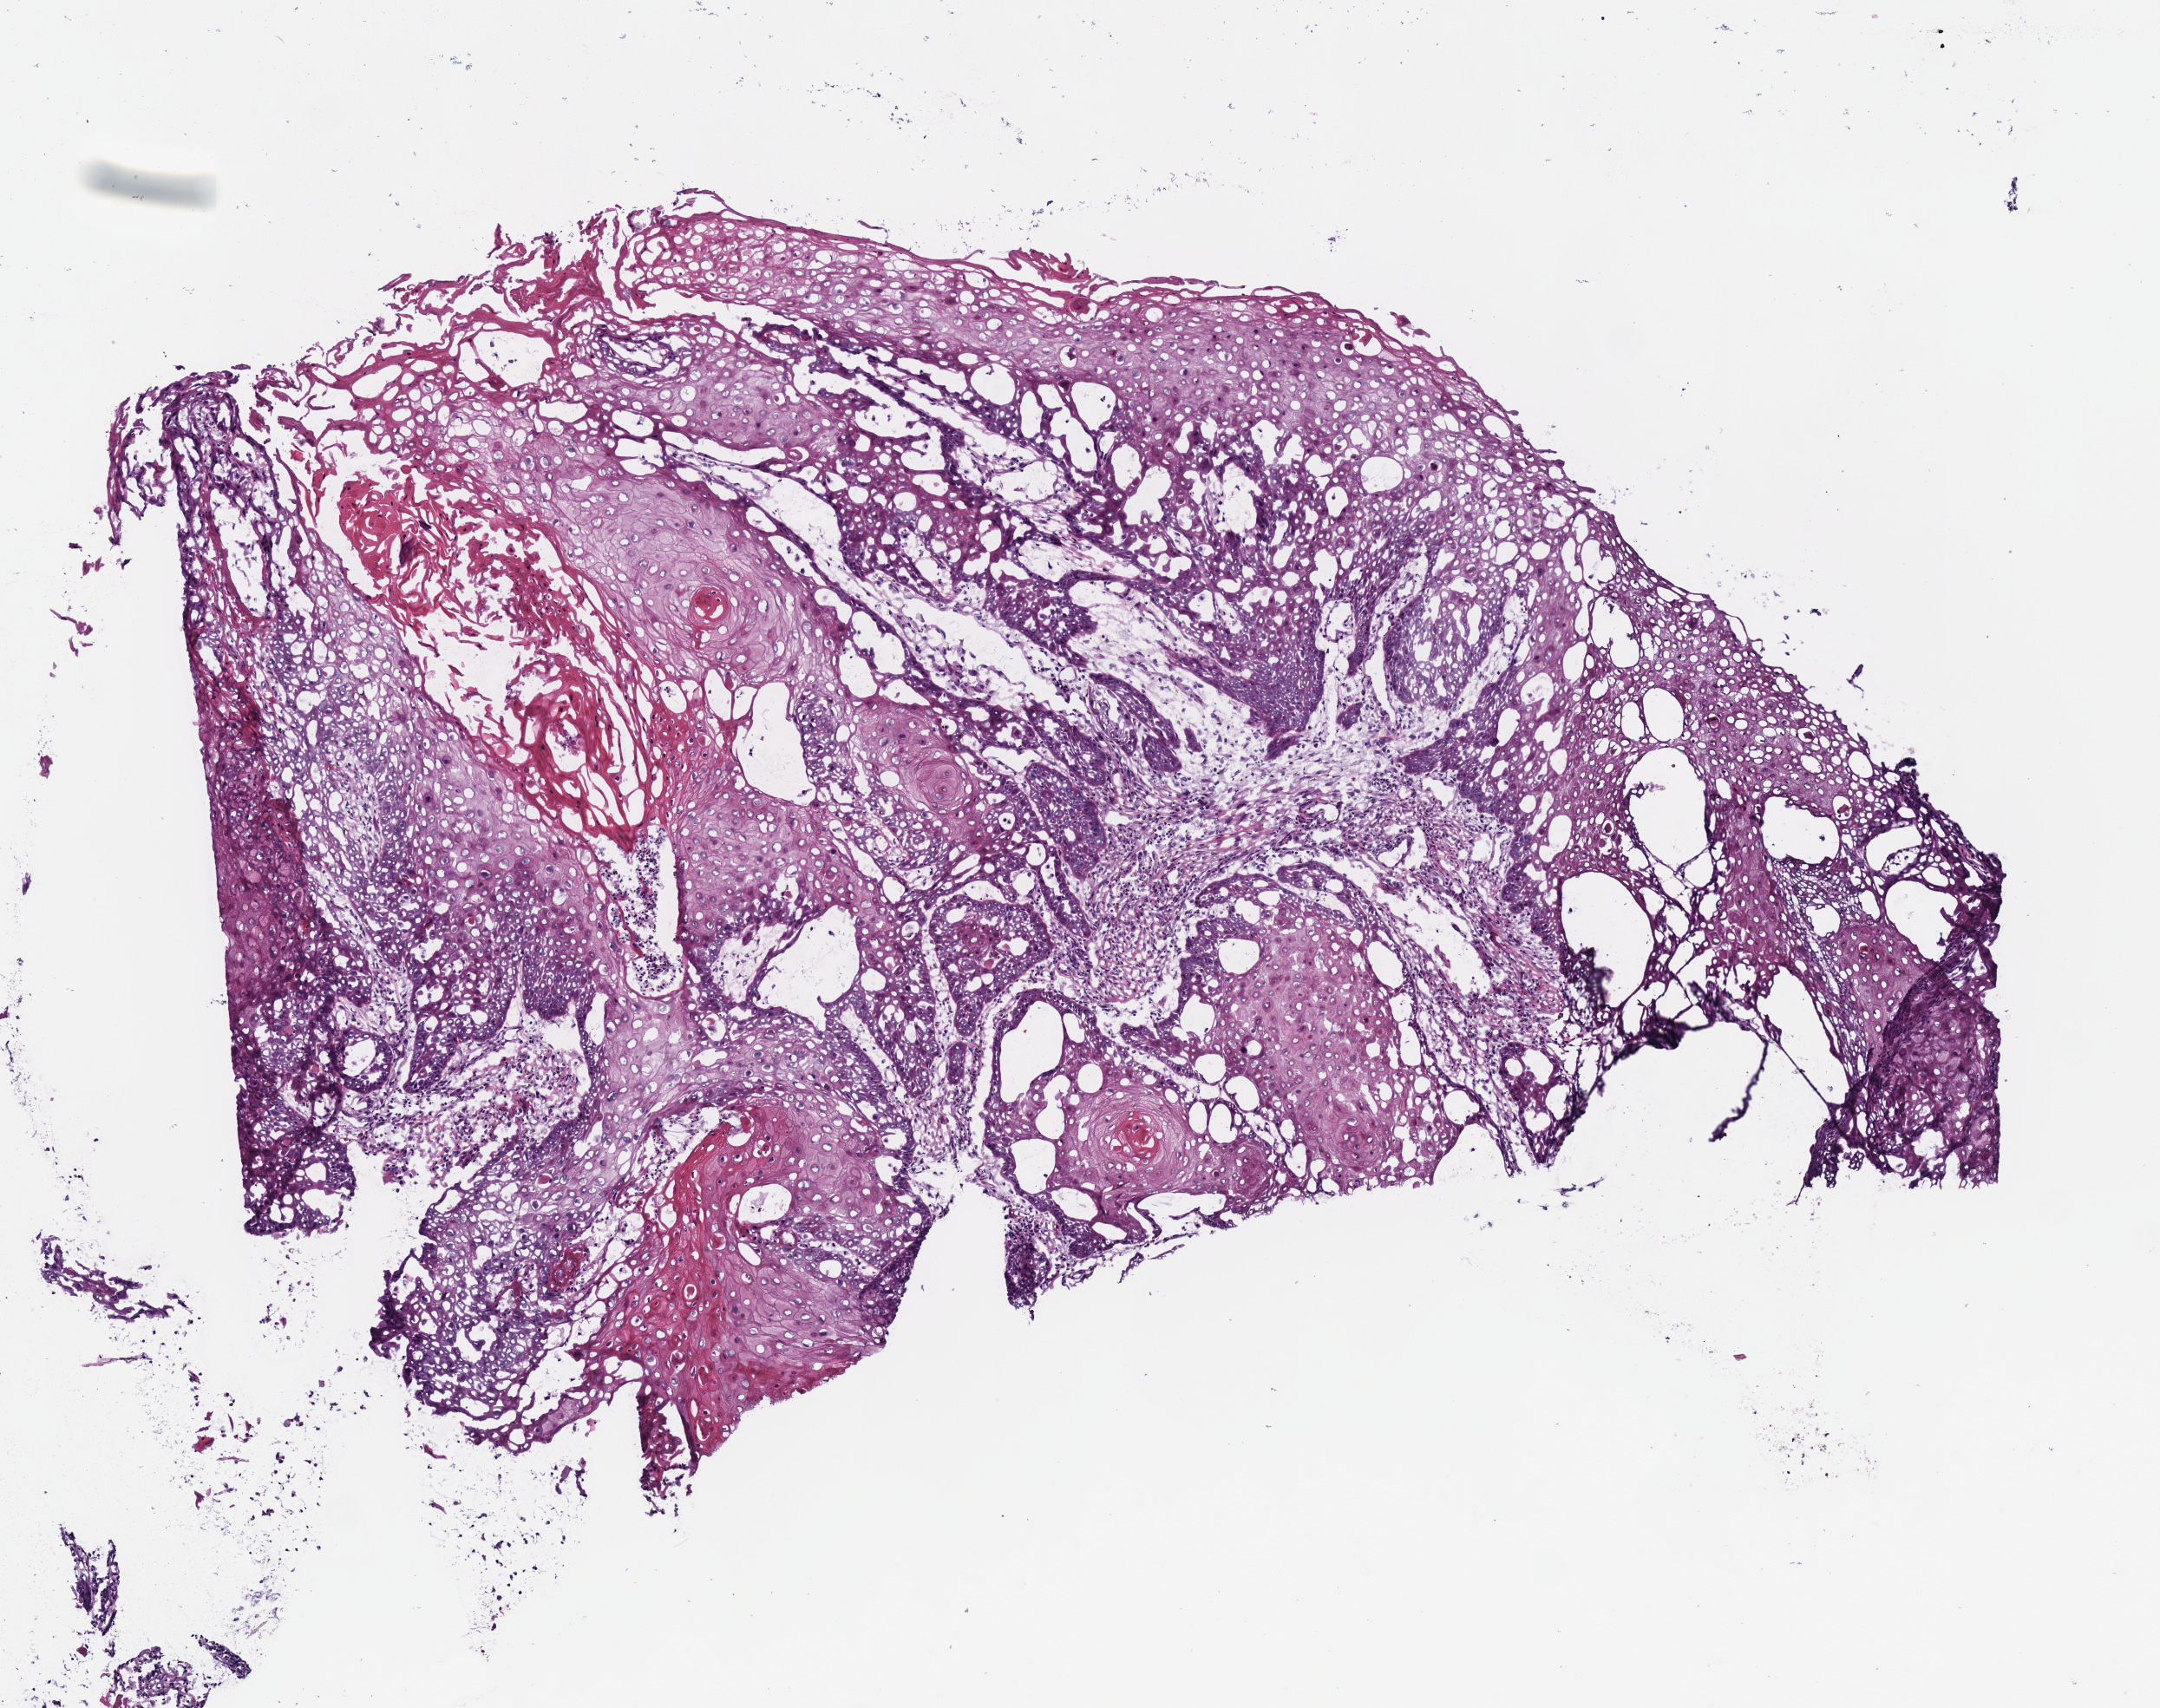
Digitized H&E tissue section (whole slide) — whole scanned area (about 4.9 x 3.9 mm, acquisition: 40x scan) shown as a low-resolution overview. Frozen section from the bottom of the tissue portion. Primary tumour sample from the head and neck. Female patient; age at initial diagnosis 43 years. Histologic grade: G2 (moderately differentiated). Slide review estimates, as recorded: tumour cells 90%, tumour nuclei 80%, normal cells 0%, stromal cells 10%, necrosis 0%.
AJCC pathologic stage: III. Diagnosis: Squamous cell carcinoma, NOS (tongue, NOS).